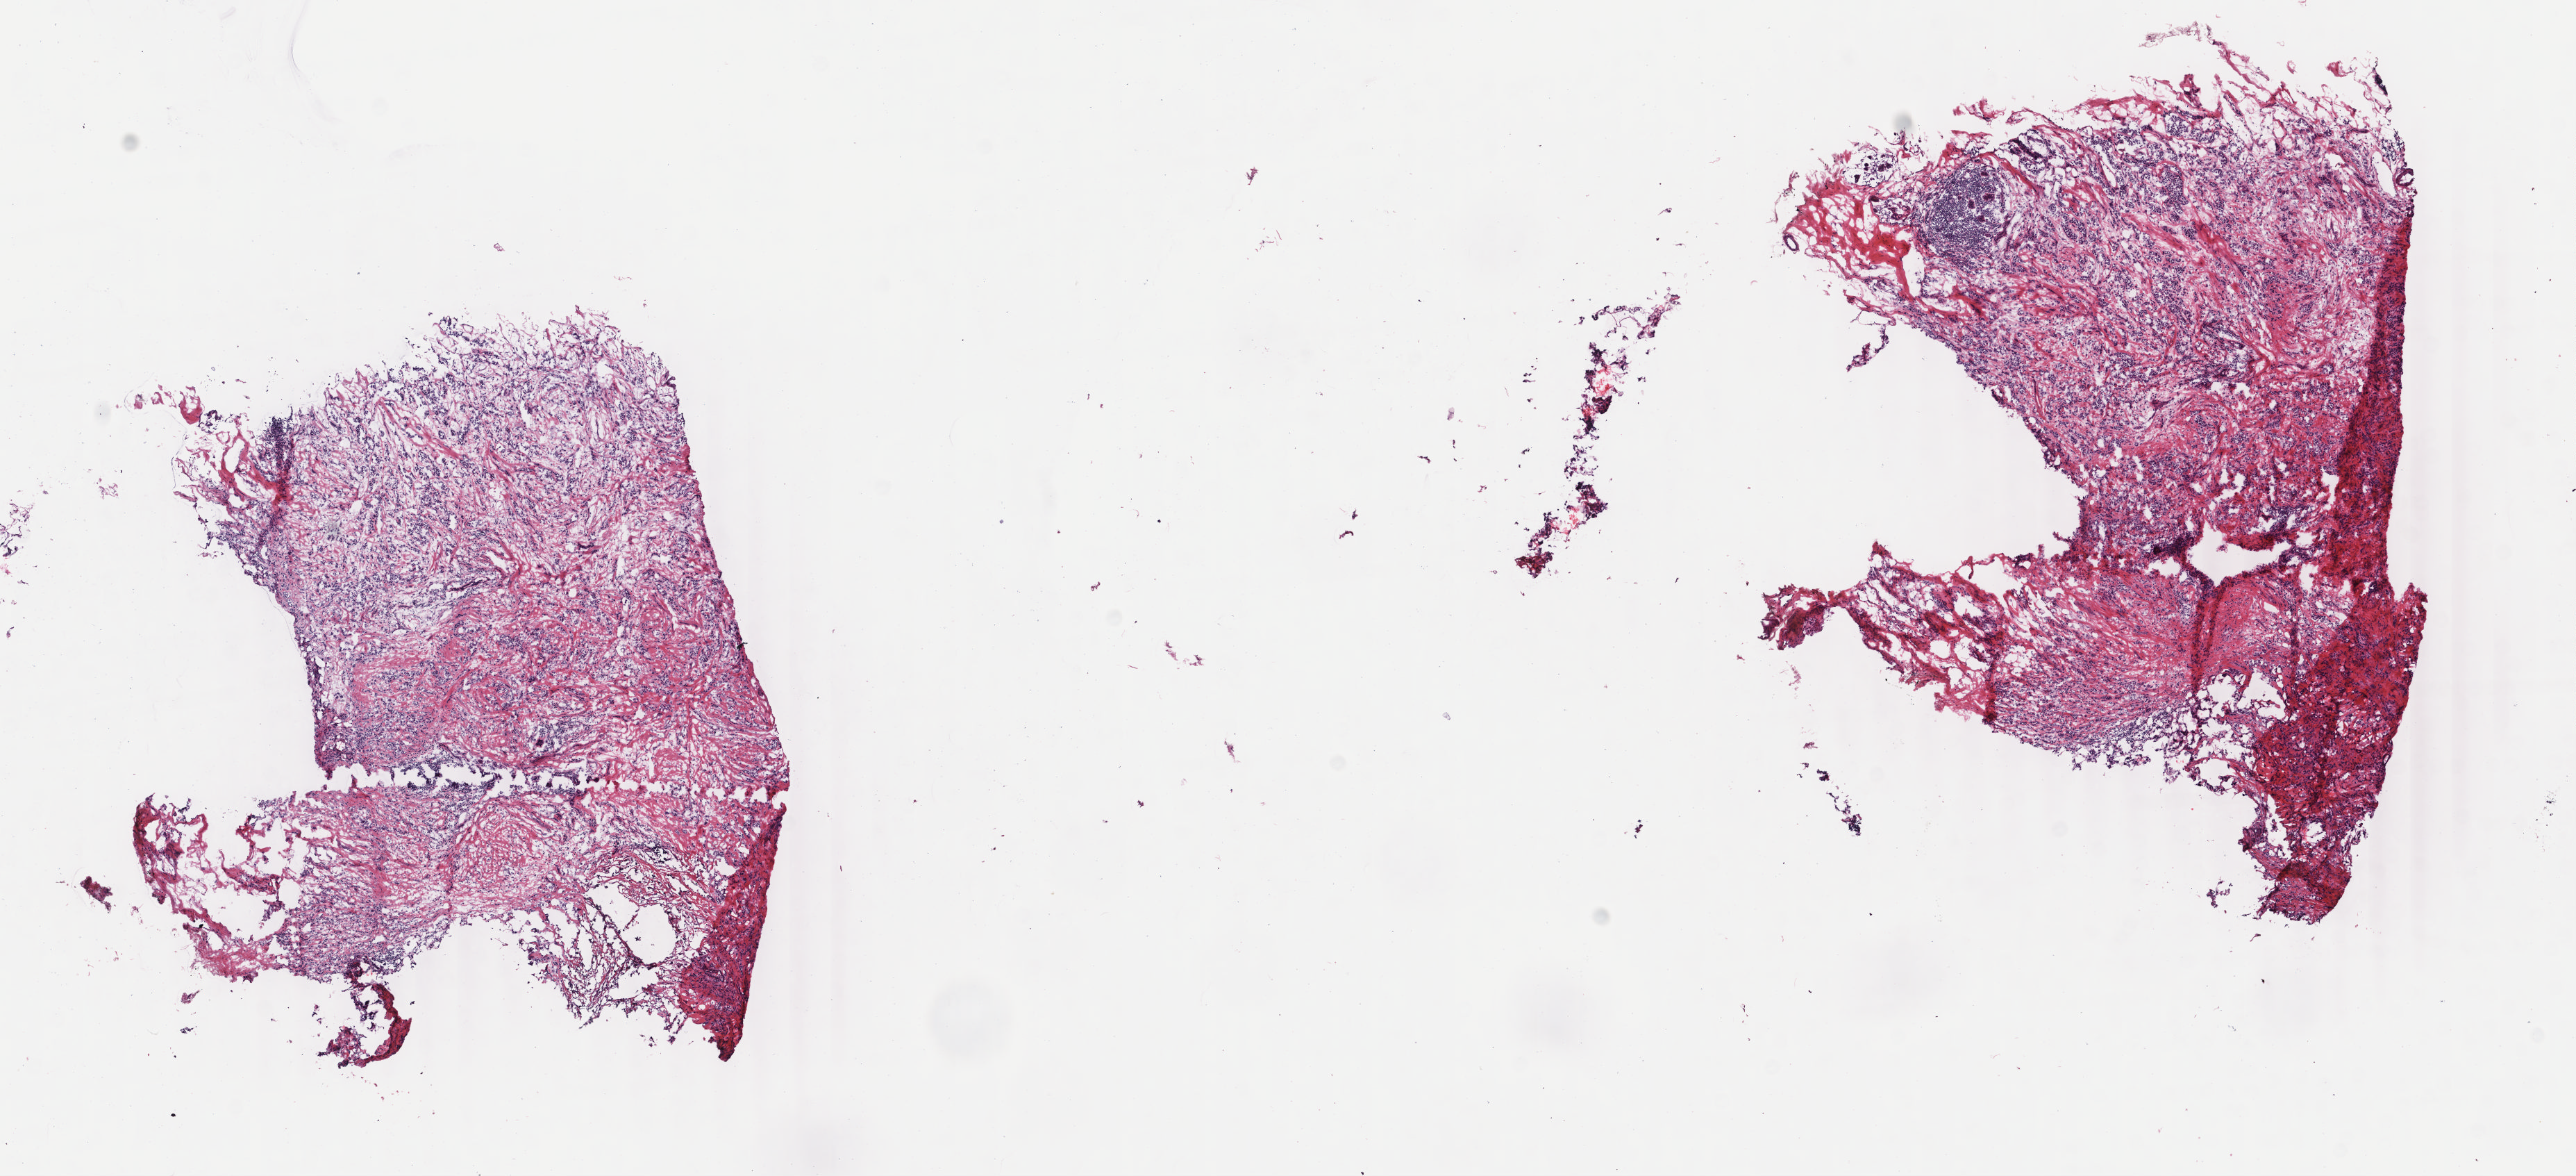
H&E-stained whole-slide image, shown as a low-resolution overview of the whole scanned area (about 14.8 x 6.7 mm, acquisition: 40x scan); frozen section; sample: primary tumour, breast. Female, age 61 years at initial diagnosis.
Diagnosis: Lobular carcinoma, NOS.